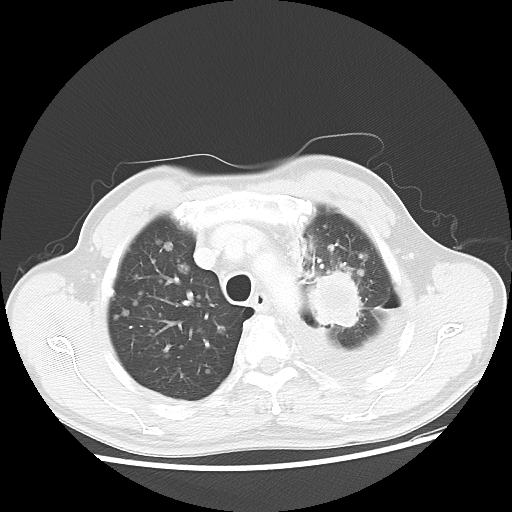
Chest CT, one axial slice. Slice 37 of 47 in the series (ordered by position). Reconstruction kernel LUNG. 100 kVp. Lung window (W 1500 / L -600 HU). 5 mm slice thickness. 512 × 512 image matrix, field of view 362 × 362 mm. Patient: male, 55 years. Case-level facts recorded for this patient, not image findings: clinical TNM (as recorded): T2 N3 M1a.
Structures marked on this image (rectangle marked by the reading radiologist):
- lung tumour (recorded histology: squamous cell carcinoma): bounding box <297,269,370,338> (left, top, right, bottom; pixels)